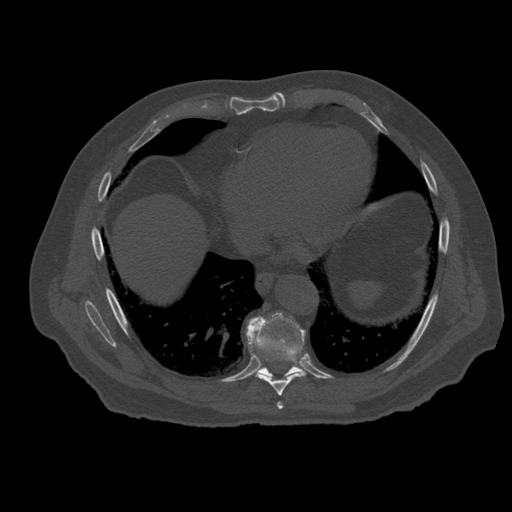
CT including the spine, one axial slice; position 332 of 399 along the scan axis; reconstruction kernel STANDARD; bone window (W 1800 / L 400 HU); 1.25 mm slice thickness; 512 × 512 image matrix, field of view 407 × 407 mm. Patient age 73 years. Case-level facts recorded for this patient, not image findings: primary cancer: prostate; vertebrae with lytic lesions (as recorded): L2.
Outlined on this slice (semi-automatic segmentation, software-assisted and operator-edited):
- T7 vertebra: bounding box [x1, y1, x2, y2] px = [277, 402, 284, 409]
- T8 vertebra: [256, 373, 303, 396]
- T9 vertebra: [247, 313, 307, 378]